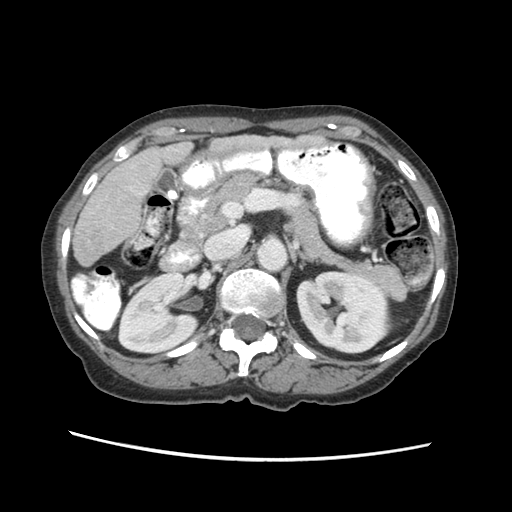
Contrast-enhanced abdominal CT (liver protocol), one axial slice; slice 20 of 63 in the series (ordered by position); 120 kVp; soft-tissue window (W 400 / L 40 HU); 2.5 mm slice thickness; 512 × 512 image matrix, field of view 340 × 340 mm. From the clinical record (not read from this slice): diagnosis: hepatocellular carcinoma (patient treated with transarterial chemoembolisation; whether this scan precedes or follows treatment is not stated here); TNM stage (as recorded): Stage-I; Child-Pugh class: B; tumour nodularity: uninodular.
Structures marked on this image (semi-automatic segmentation, software-assisted and operator-edited):
- liver parenchyma outside the tumour (the mass and vessels are separate outlines, so this box may not span the whole liver): bounding box (x1, y1, x2, y2) in pixels: (72, 132, 270, 264)
- liver vessels: (110, 222, 113, 225)